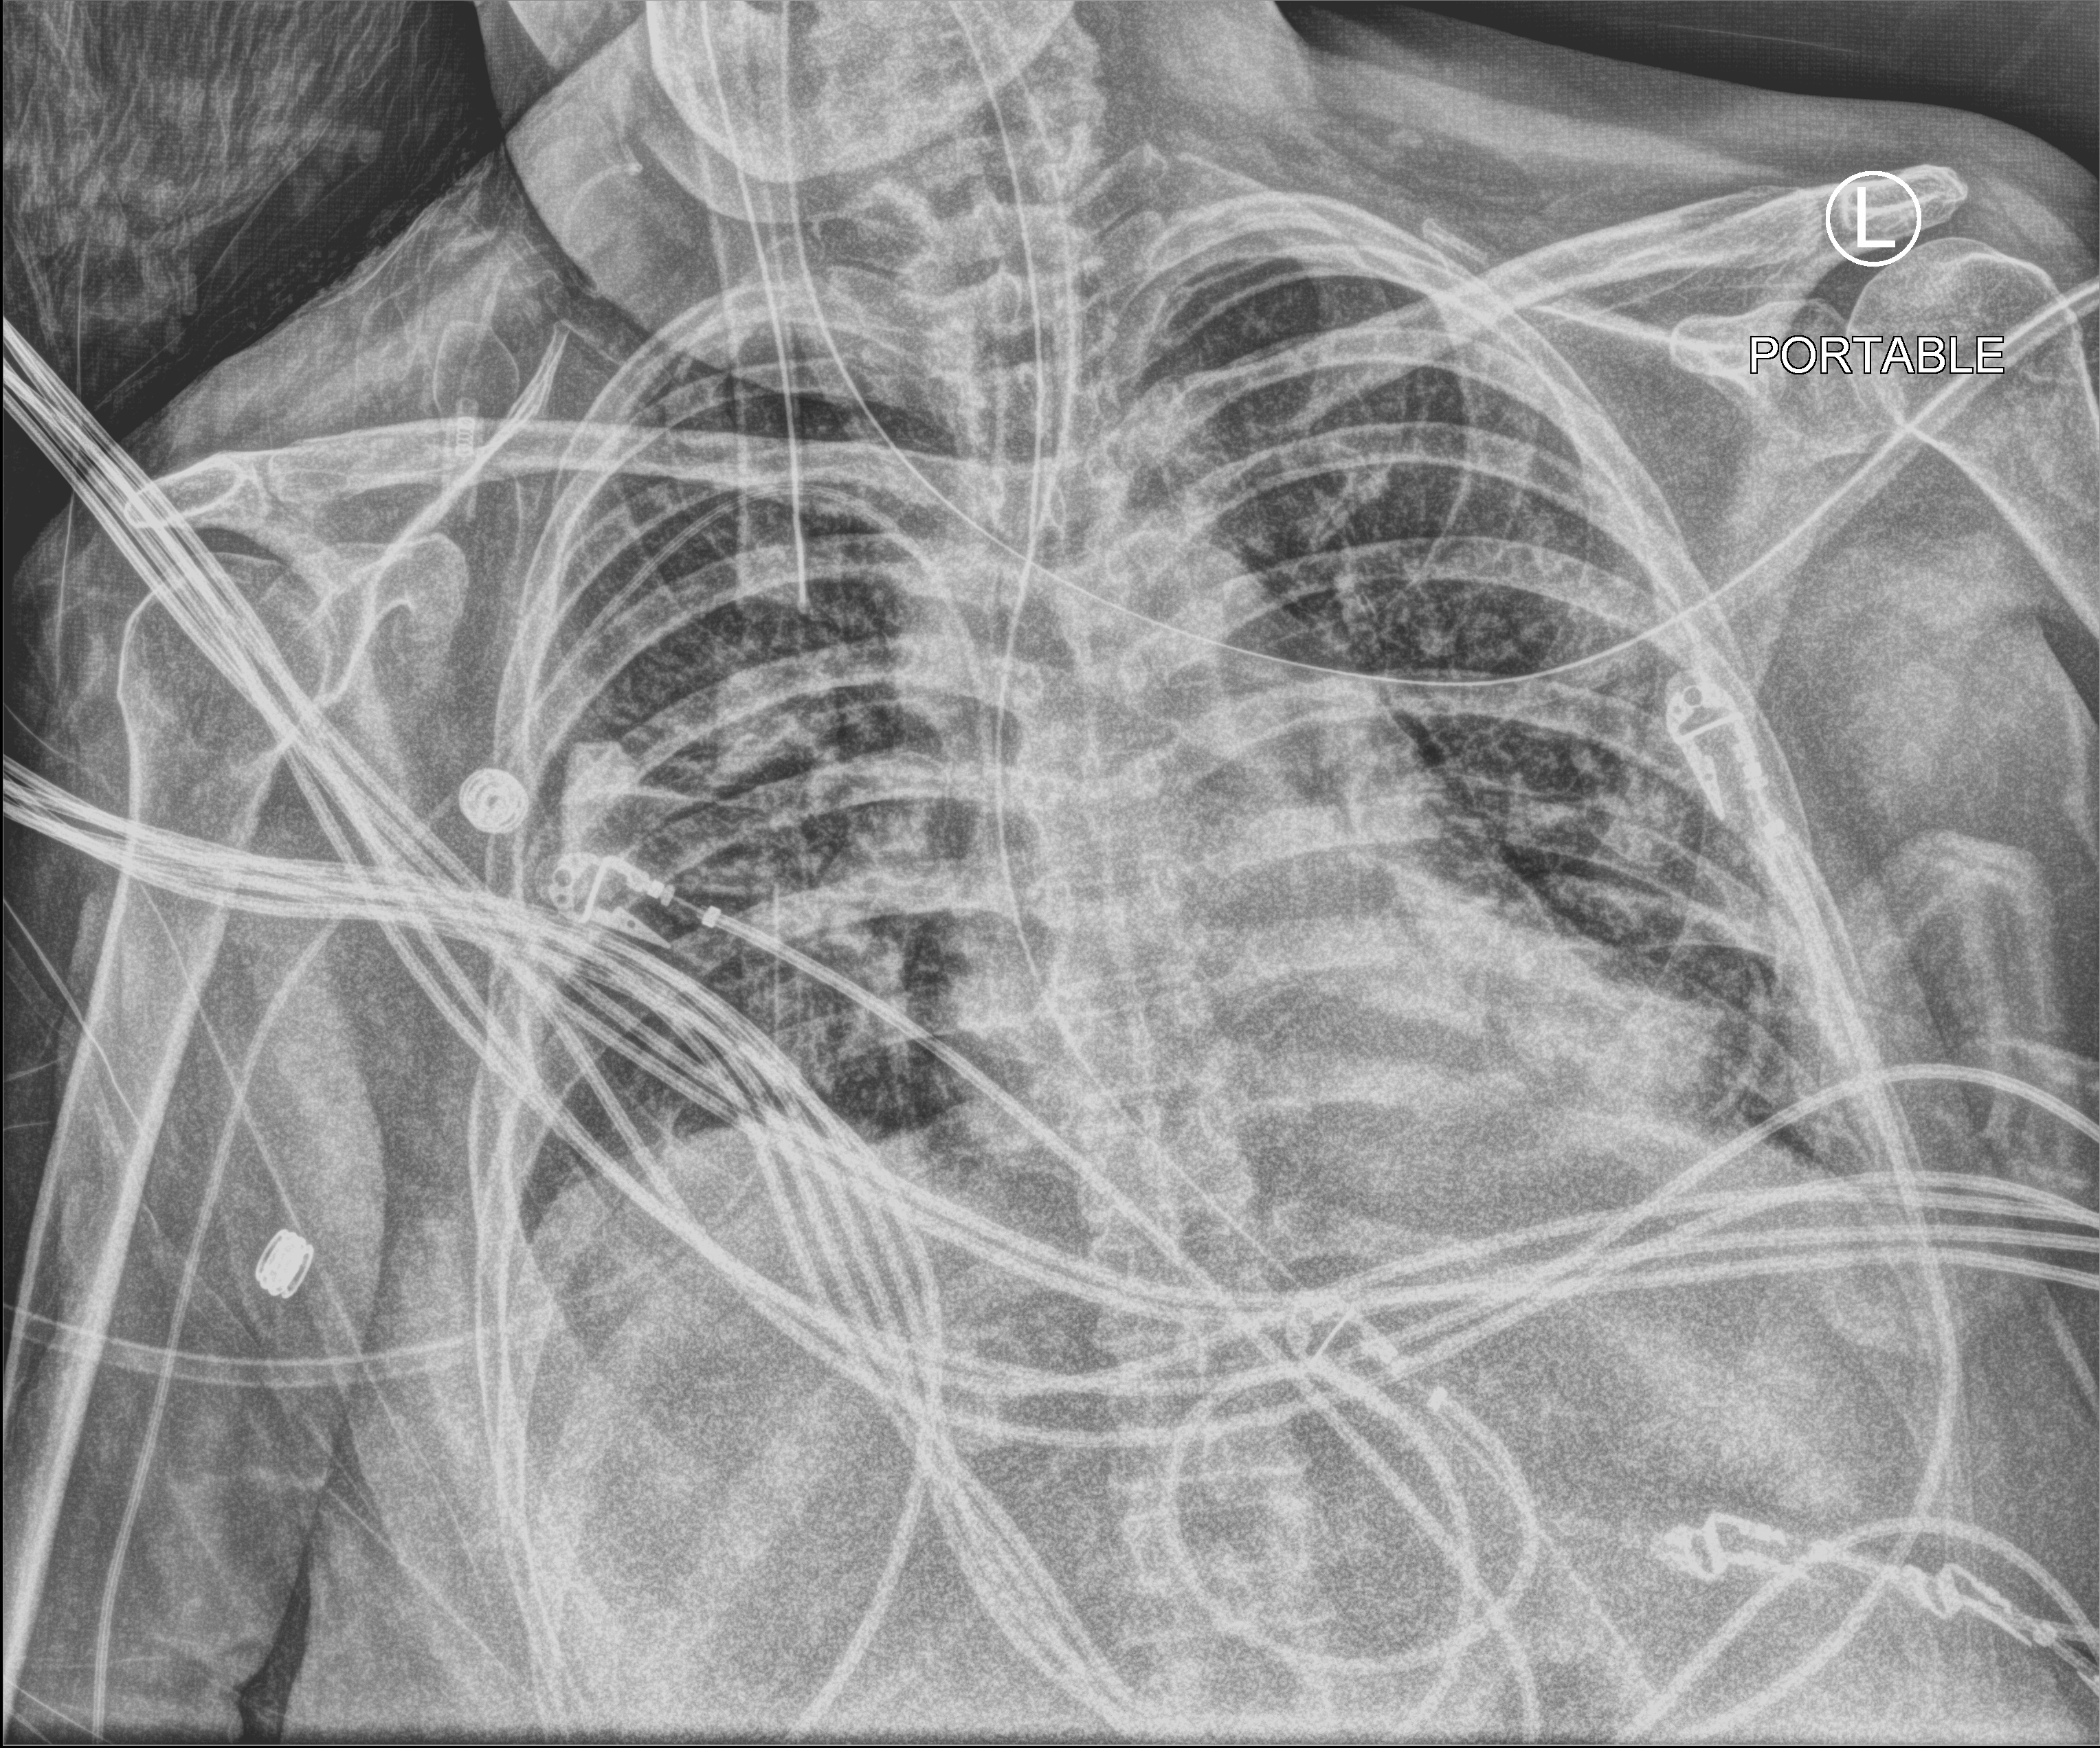
Portable chest radiograph; anteroposterior (AP) projection. Female patient hospitalised with COVID-19, age 60–74 years.
From the hospital-stay record, not from the radiograph (when in the stay this image was taken is not recorded): length of hospital stay: 9 days; mechanically ventilated during this hospital stay: yes; admitted to intensive care during this hospital stay: yes.